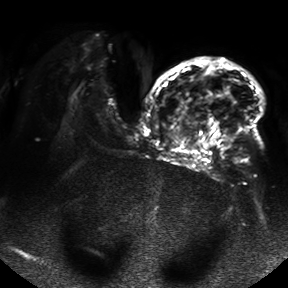
Breast MRI, one axial slice; slice 26 of 50 in the series (ordered by position); diffusion-weighted series; image 2 of 4 stored at this slice position (different b-values; order by instance number); 1.5 T; 288 × 288 image matrix, field of view 390 × 390 mm. Female patient.
Annotated regions visible in this slice (expert manual segmentation):
- tumour on diffusion-weighted imaging: bounding box <222,135,233,143> (left, top, right, bottom; pixels)